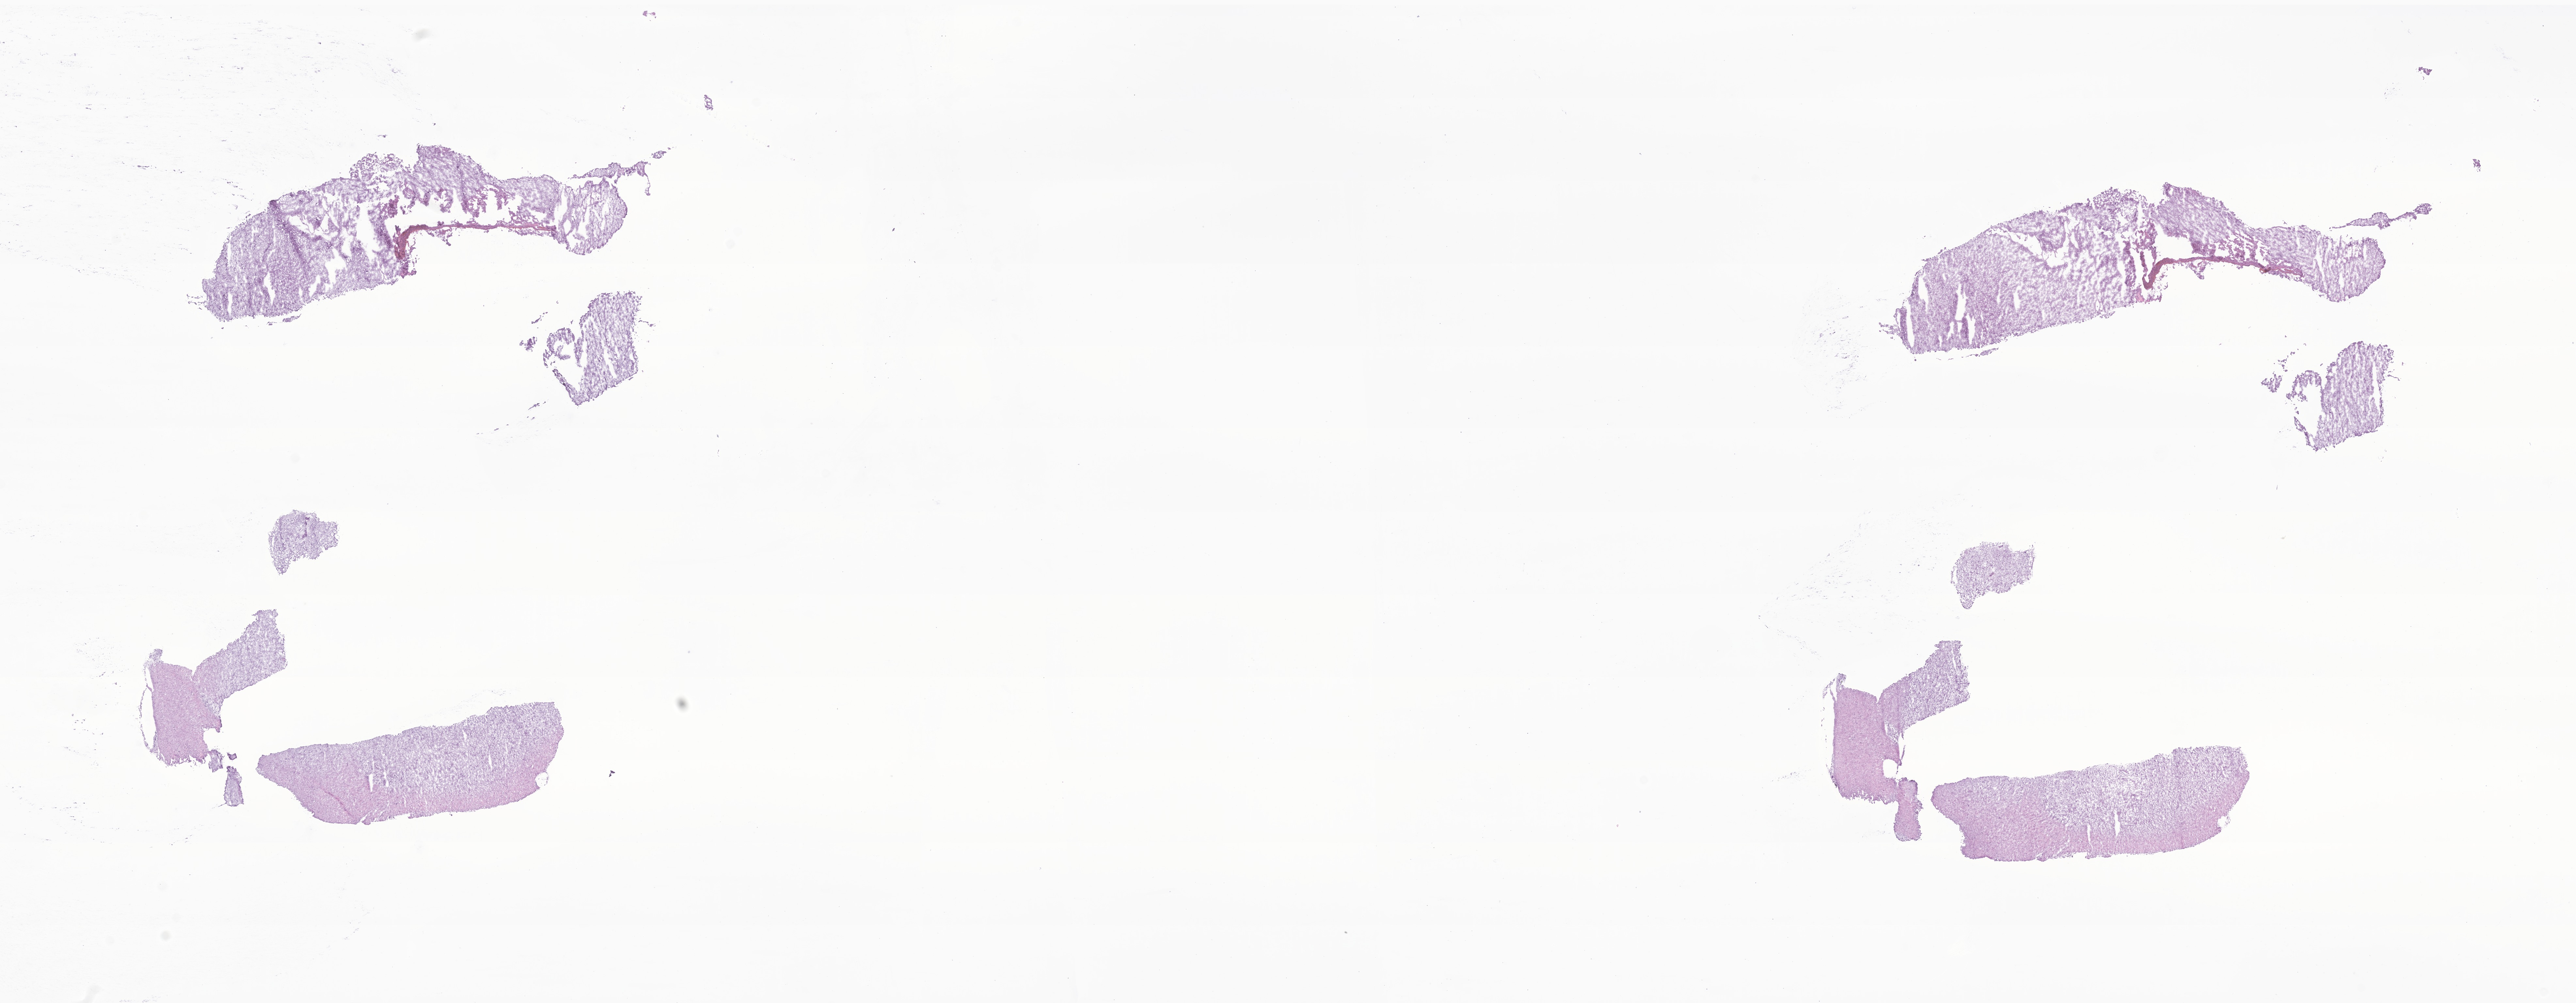
Digitized H&E-stained section of tumor tissue from the brain — whole scanned area (about 33.3 x 13.0 mm) shown as a low-resolution overview. Frozen section (OCT-embedded). Patient: male, age 722 days (about 2.0 years).
* diagnosis: Oligoastrocytoma, NOS